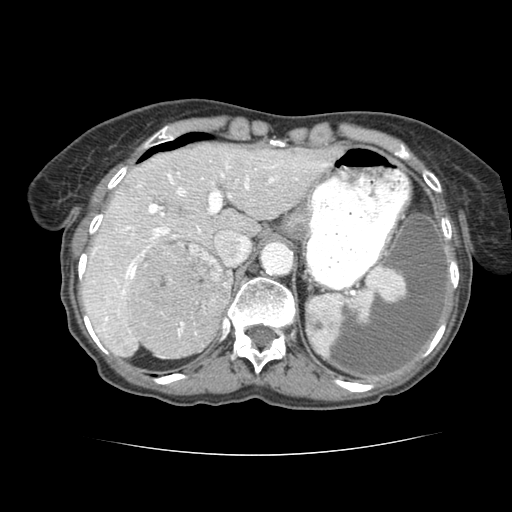
Contrast-enhanced abdominal CT (liver protocol), one axial slice. Position 56 of 77 along the scan axis. 120 kVp. Soft-tissue window (W 400 / L 40 HU). 512 × 512 image matrix, field of view 340 × 340 mm. Case-level facts recorded for this patient, not image findings: diagnosis: hepatocellular carcinoma (patient treated with transarterial chemoembolisation; whether this scan precedes or follows treatment is not stated here); TNM stage (as recorded): Stage-I; Child-Pugh class: A; tumour differentiation: well differentiated; tumour size: 7.6 cm.
Annotated regions visible in this slice (semi-automatic segmentation, software-assisted and operator-edited):
- liver parenchyma outside the tumour (the mass and vessels are separate outlines, so this box may not span the whole liver): bounding box [x1, y1, x2, y2] px = [80, 144, 328, 352]
- mass: [126, 238, 229, 353]
- liver vessels: [100, 168, 317, 328]